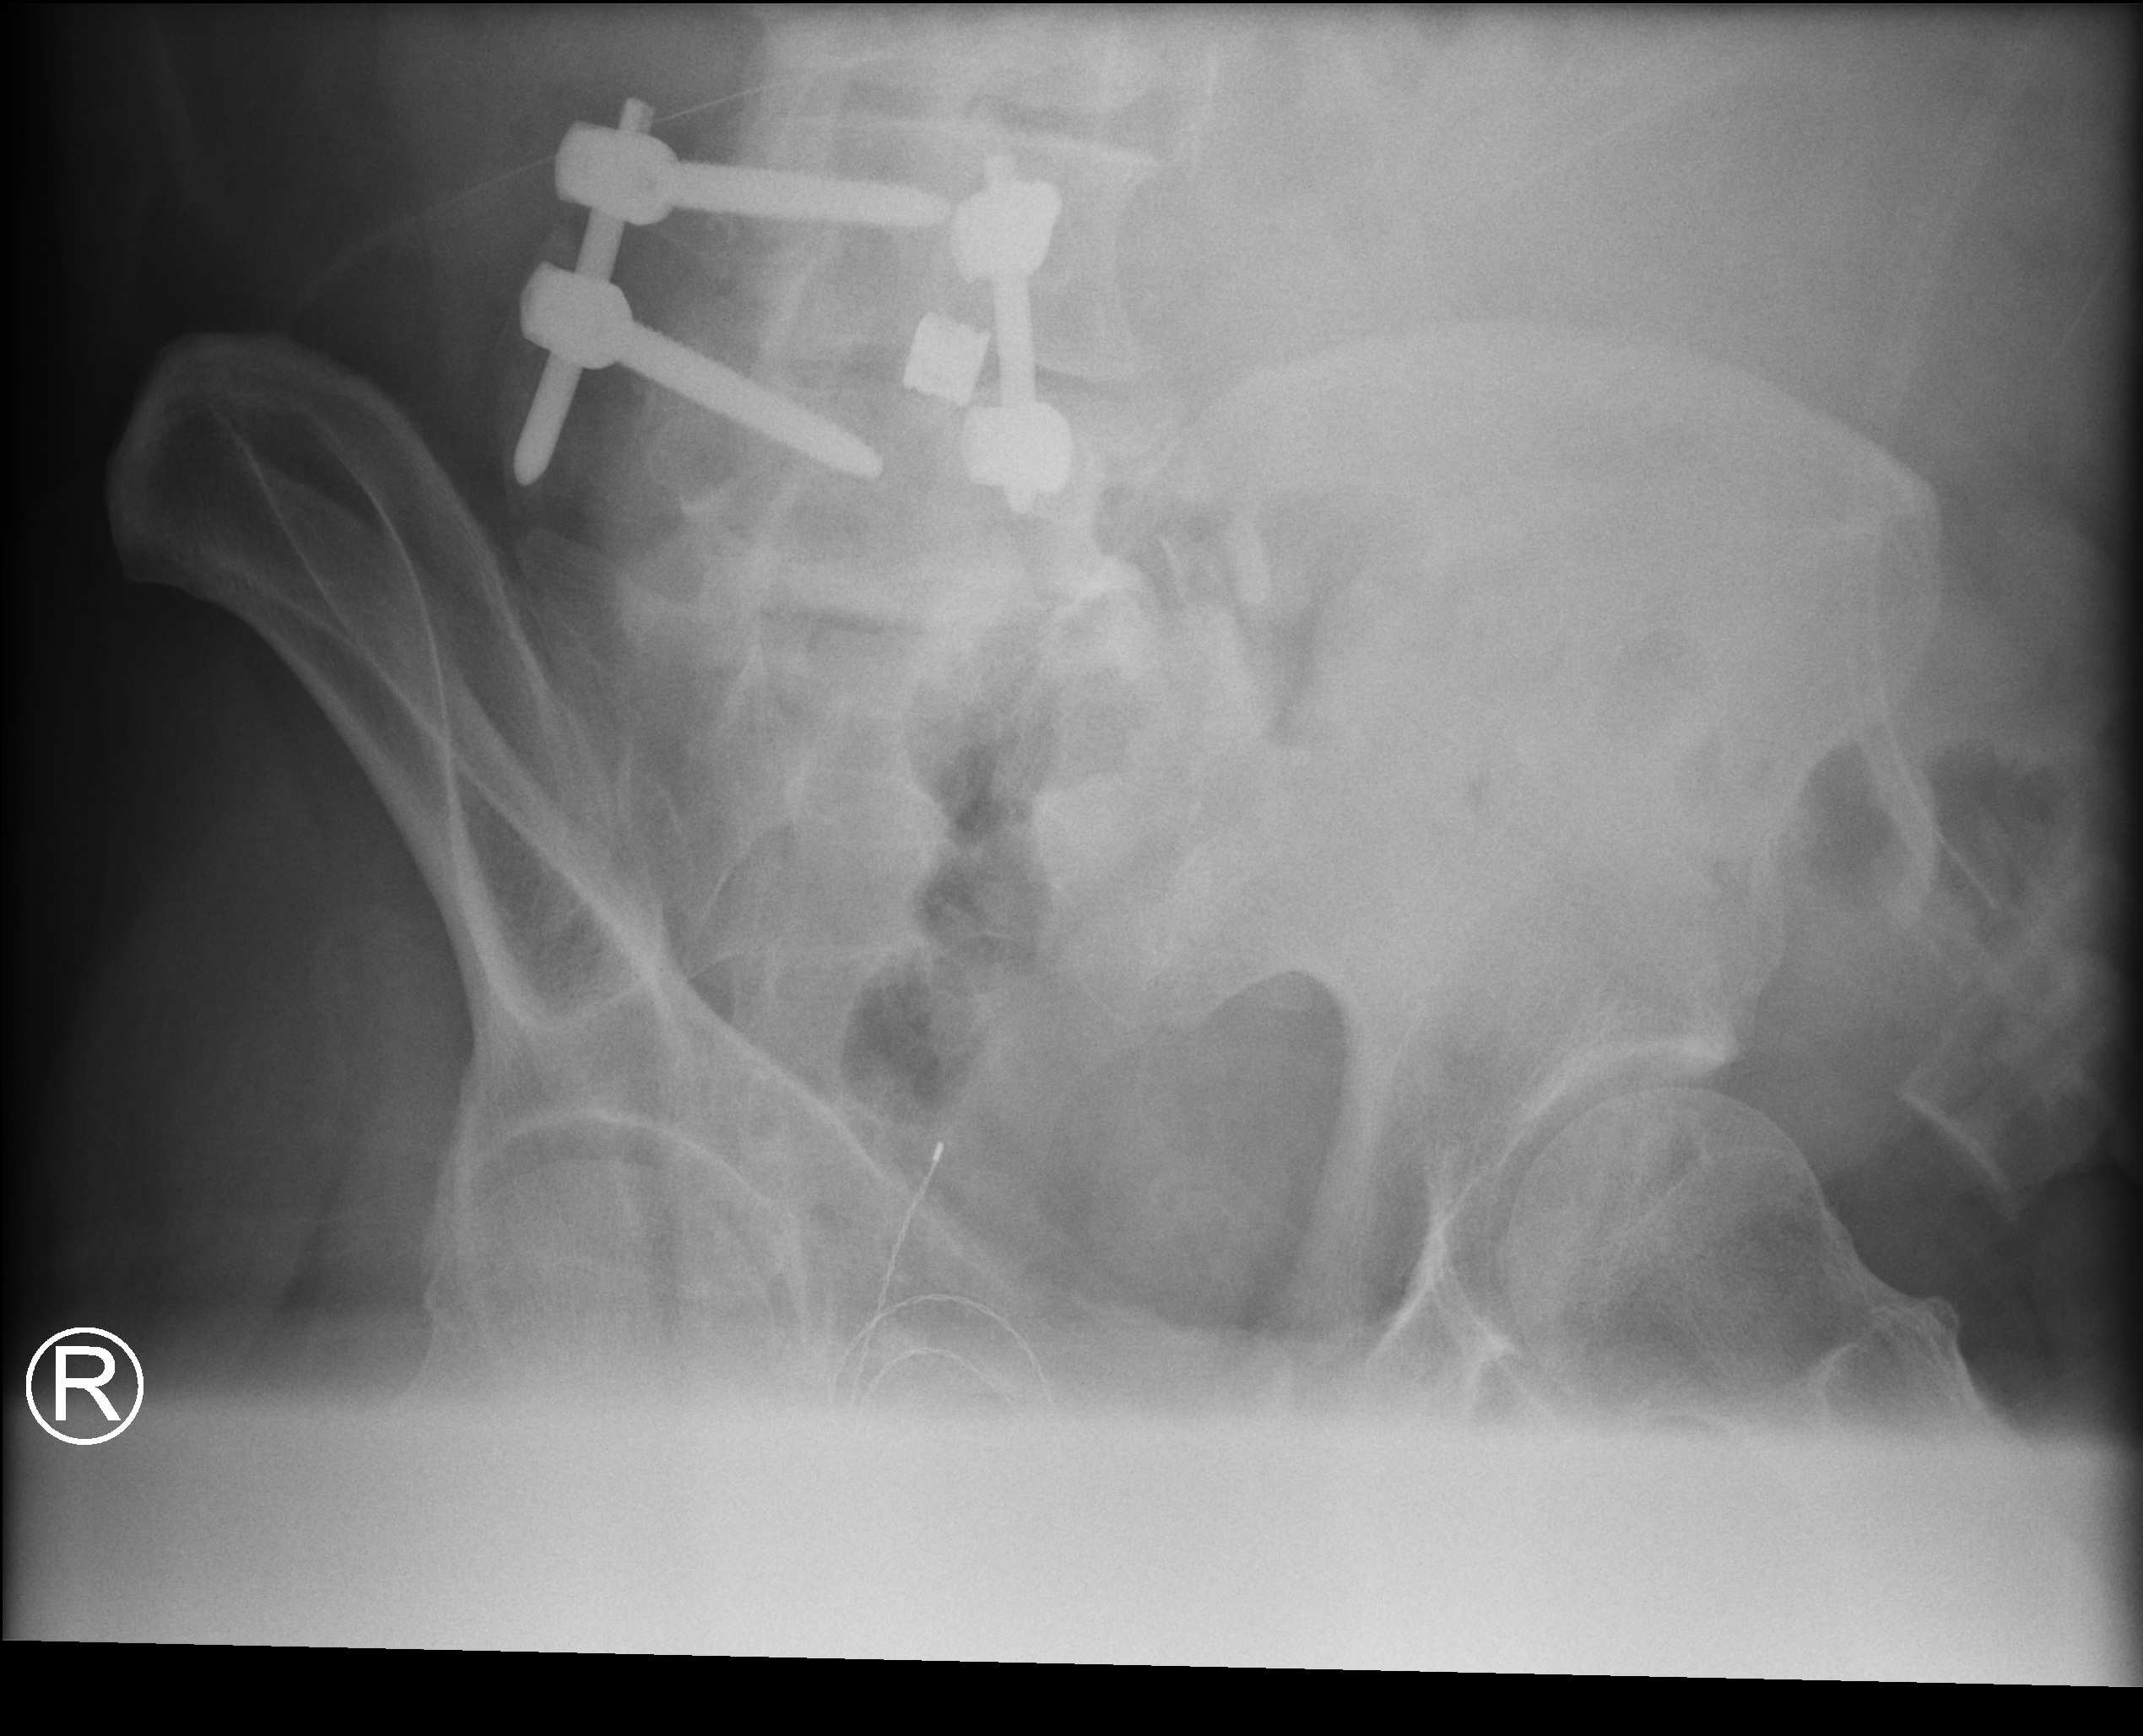
Bedside abdomen radiograph (computed radiography), anteroposterior (AP) projection. Male patient hospitalised with COVID-19, age 60–74 years.
From the hospital-stay record, not from the radiograph (when in the stay this image was taken is not recorded):
- admitted to intensive care during this hospital stay: yes
- COPD (admission record): no